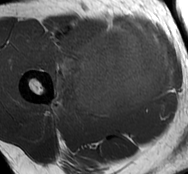
MRI of an extremity soft-tissue mass, one axial slice. MR volume resampled by the dataset authors to the PET/CT grid (not the native acquisition matrix). 3.27 mm slice thickness. 188 × 174 image matrix. Male patient. From the clinical record (not read from this slice): histological type: undifferentiated - pleiomorphic; grade: high; site of the primary tumour: right thigh.
Outlined on this slice (expert contour drawn on MRI and transferred to this co-registered scan by the dataset authors):
- gross tumour volume including surrounding oedema: box from (x=52, y=23) to (x=174, y=116) px
- gross tumour volume (mass): (x=72, y=24)–(x=174, y=116)